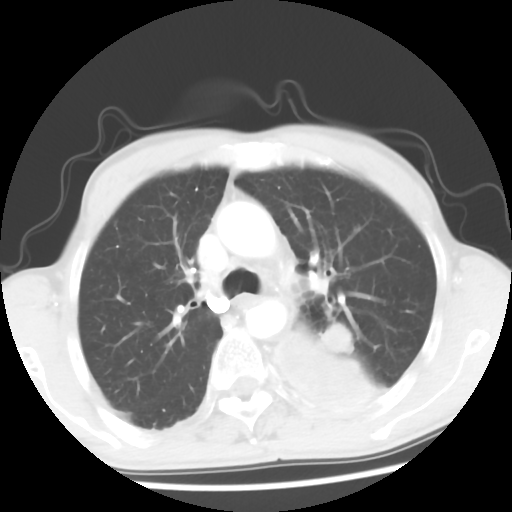
Chest CT, one axial slice; slice 39 of 56 in the series (ordered by position); reconstruction kernel STANDARD; lung window (W 1500 / L -600 HU); 512 × 512 image matrix. Male patient, age 60 years. From the clinical record (not read from this slice): clinical TNM (as recorded): T4 N0 M0.
Structures marked on this image (rectangle marked by the reading radiologist):
- lung tumour (recorded histology: squamous cell carcinoma): bounding box [x1, y1, x2, y2] px = [272, 321, 394, 434]